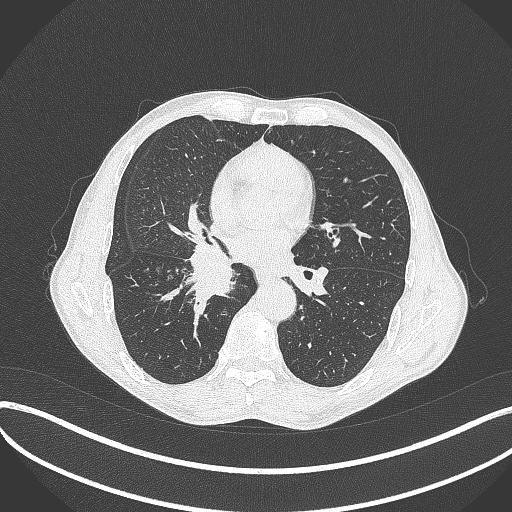
Chest CT, one axial slice. Slice 212 of 481 in the series (ordered by position). Reconstruction kernel B70f. Lung window (W 1500 / L -600 HU). 512 × 512 image matrix, field of view 400 × 400 mm. Male patient, age 65 years. Case-level facts recorded for this patient, not image findings: clinical TNM (as recorded): T2a N0 M0; histopathological grade: G2.
Outlined on this slice (bounding box drawn by a radiologist):
- lung tumour (recorded histology: squamous cell carcinoma): bounding box [x1, y1, x2, y2] px = [185, 244, 238, 307]